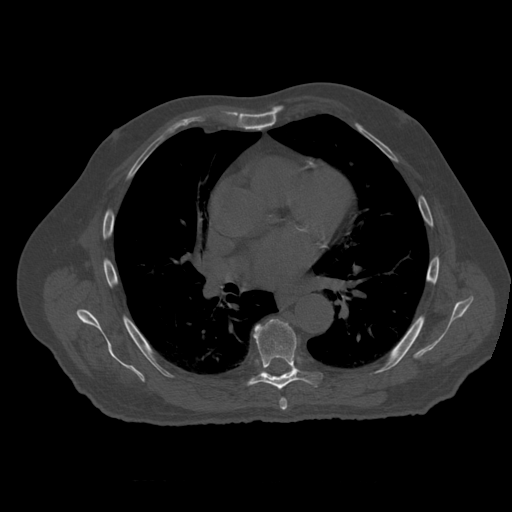
CT including the spine, one axial slice. Position 364 of 399 along the scan axis. 120 kVp. Bone window (W 1800 / L 400 HU). 512 × 512 image matrix, field of view 407 × 407 mm. Patient age 73 years. Case-level facts recorded for this patient, not image findings: primary cancer: prostate.
Annotated regions visible in this slice (semi-automatically segmented with operator editing):
- T6 vertebra: bounding box (x1, y1, x2, y2) in pixels: (280, 398, 288, 411)
- T7 vertebra: (248, 320, 324, 390)